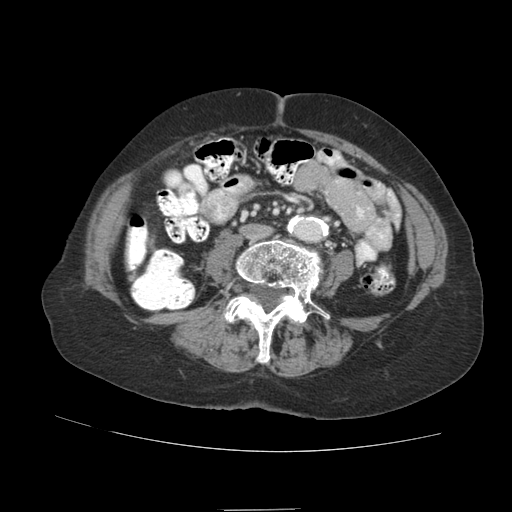
Contrast-enhanced abdominal CT (liver protocol), one axial slice. Position 5 of 89 along the scan axis. Reconstruction kernel STANDARD. Soft-tissue window (W 400 / L 40 HU). 512 × 512 image matrix, field of view 360 × 360 mm. Case-level facts recorded for this patient, not image findings: diagnosis: hepatocellular carcinoma (patient treated with transarterial chemoembolisation; whether this scan precedes or follows treatment is not stated here); TNM stage (as recorded): Stage-II; Child-Pugh class: A; tumour differentiation: moderately differentiated; tumour nodularity: multinodular.
Annotated regions visible in this slice (semi-automatic segmentation, software-assisted and operator-edited):
- liver parenchyma outside the tumour (the mass and vessels are separate outlines, so this box may not span the whole liver): box from (x=128, y=228) to (x=146, y=251) px
- liver vessels: (x=128, y=228)–(x=146, y=263)